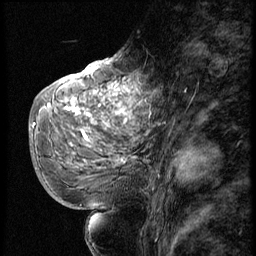
Breast MRI (dynamic contrast-enhanced), one sagittal slice; slice 31 of 56 in the series (ordered by position); 3 images stored at this slice position (order not interpretable as contrast timing); 1.5 T; TE 4.2 ms, TR 9 ms; 2.5 mm slice thickness; 256 × 256 image matrix, field of view 180 × 180 mm. Female patient, age 51 years. Case-level facts recorded for this patient, not image findings: setting: breast cancer imaged before/during neoadjuvant chemotherapy; receptor status: triple-negative.
Structures marked on this image (semi-automatically segmented with operator editing):
- analysis volume of interest (the breast-tissue region the enhancement analysis was run in; not a lesion): bounding box (x1, y1, x2, y2) in pixels: (52, 66, 142, 179)
- tumour enhancement mask (voxels above the 140 % enhancement threshold inside the analysis volume of interest): (65, 68, 137, 139)